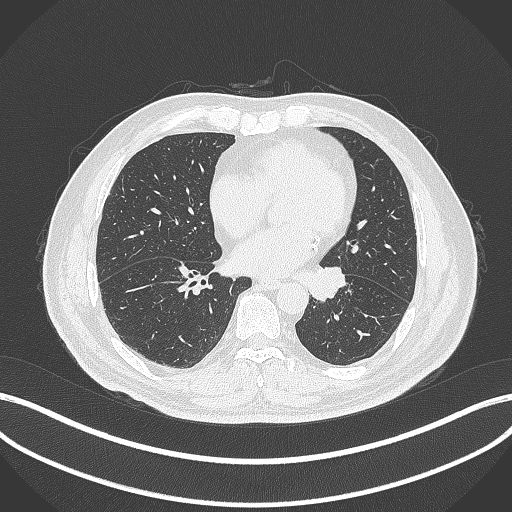
Chest CT, one axial slice; position 116 of 312 along the scan axis; reconstruction kernel B70f; lung window (W 1500 / L -600 HU); 1 mm slice thickness; 512 × 512 image matrix, field of view 400 × 400 mm. Male patient, age 71 years. From the clinical record (not read from this slice): clinical TNM (as recorded): T1b N0 M0.
Annotated regions visible in this slice (rectangle marked by the reading radiologist):
- lung tumour (recorded histology: squamous cell carcinoma): box from (x=309, y=263) to (x=351, y=302) px